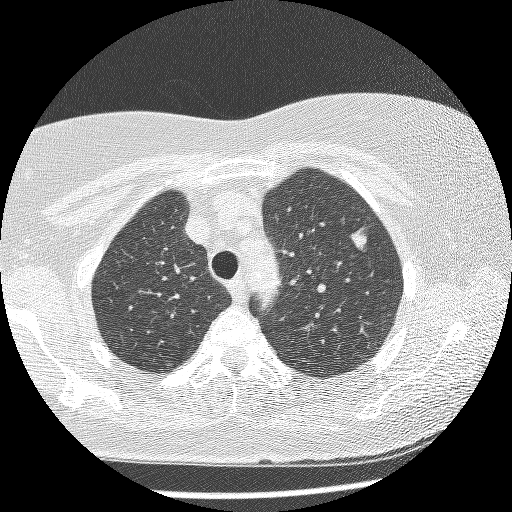
Axial slice from a low-dose chest CT screening exam; first (baseline) screen; lung window (W 1500 / L -600 HU); 1.25 mm slice thickness; lung (sharp) reconstruction kernel (BONE); 120 kVp; slice 183 of 241 in the series; 512 × 512 image matrix. Female participant, aged 61 years at enrolment.
Expert-annotated lung lesion, bounding box (x1, y1, x2, y2) in pixels: (329, 220, 383, 268). The screening reader recorded 4 non-calcified nodules or masses ≥4 mm on this exam; which of them this box marks is not recorded. Later outcome: lung cancer diagnosed 111 days after this screen — bronchiolo-alveolar adenocarcinoma, NOS, left upper lobe, stage IV (AJCC 6th edition), 10 mm at pathology.